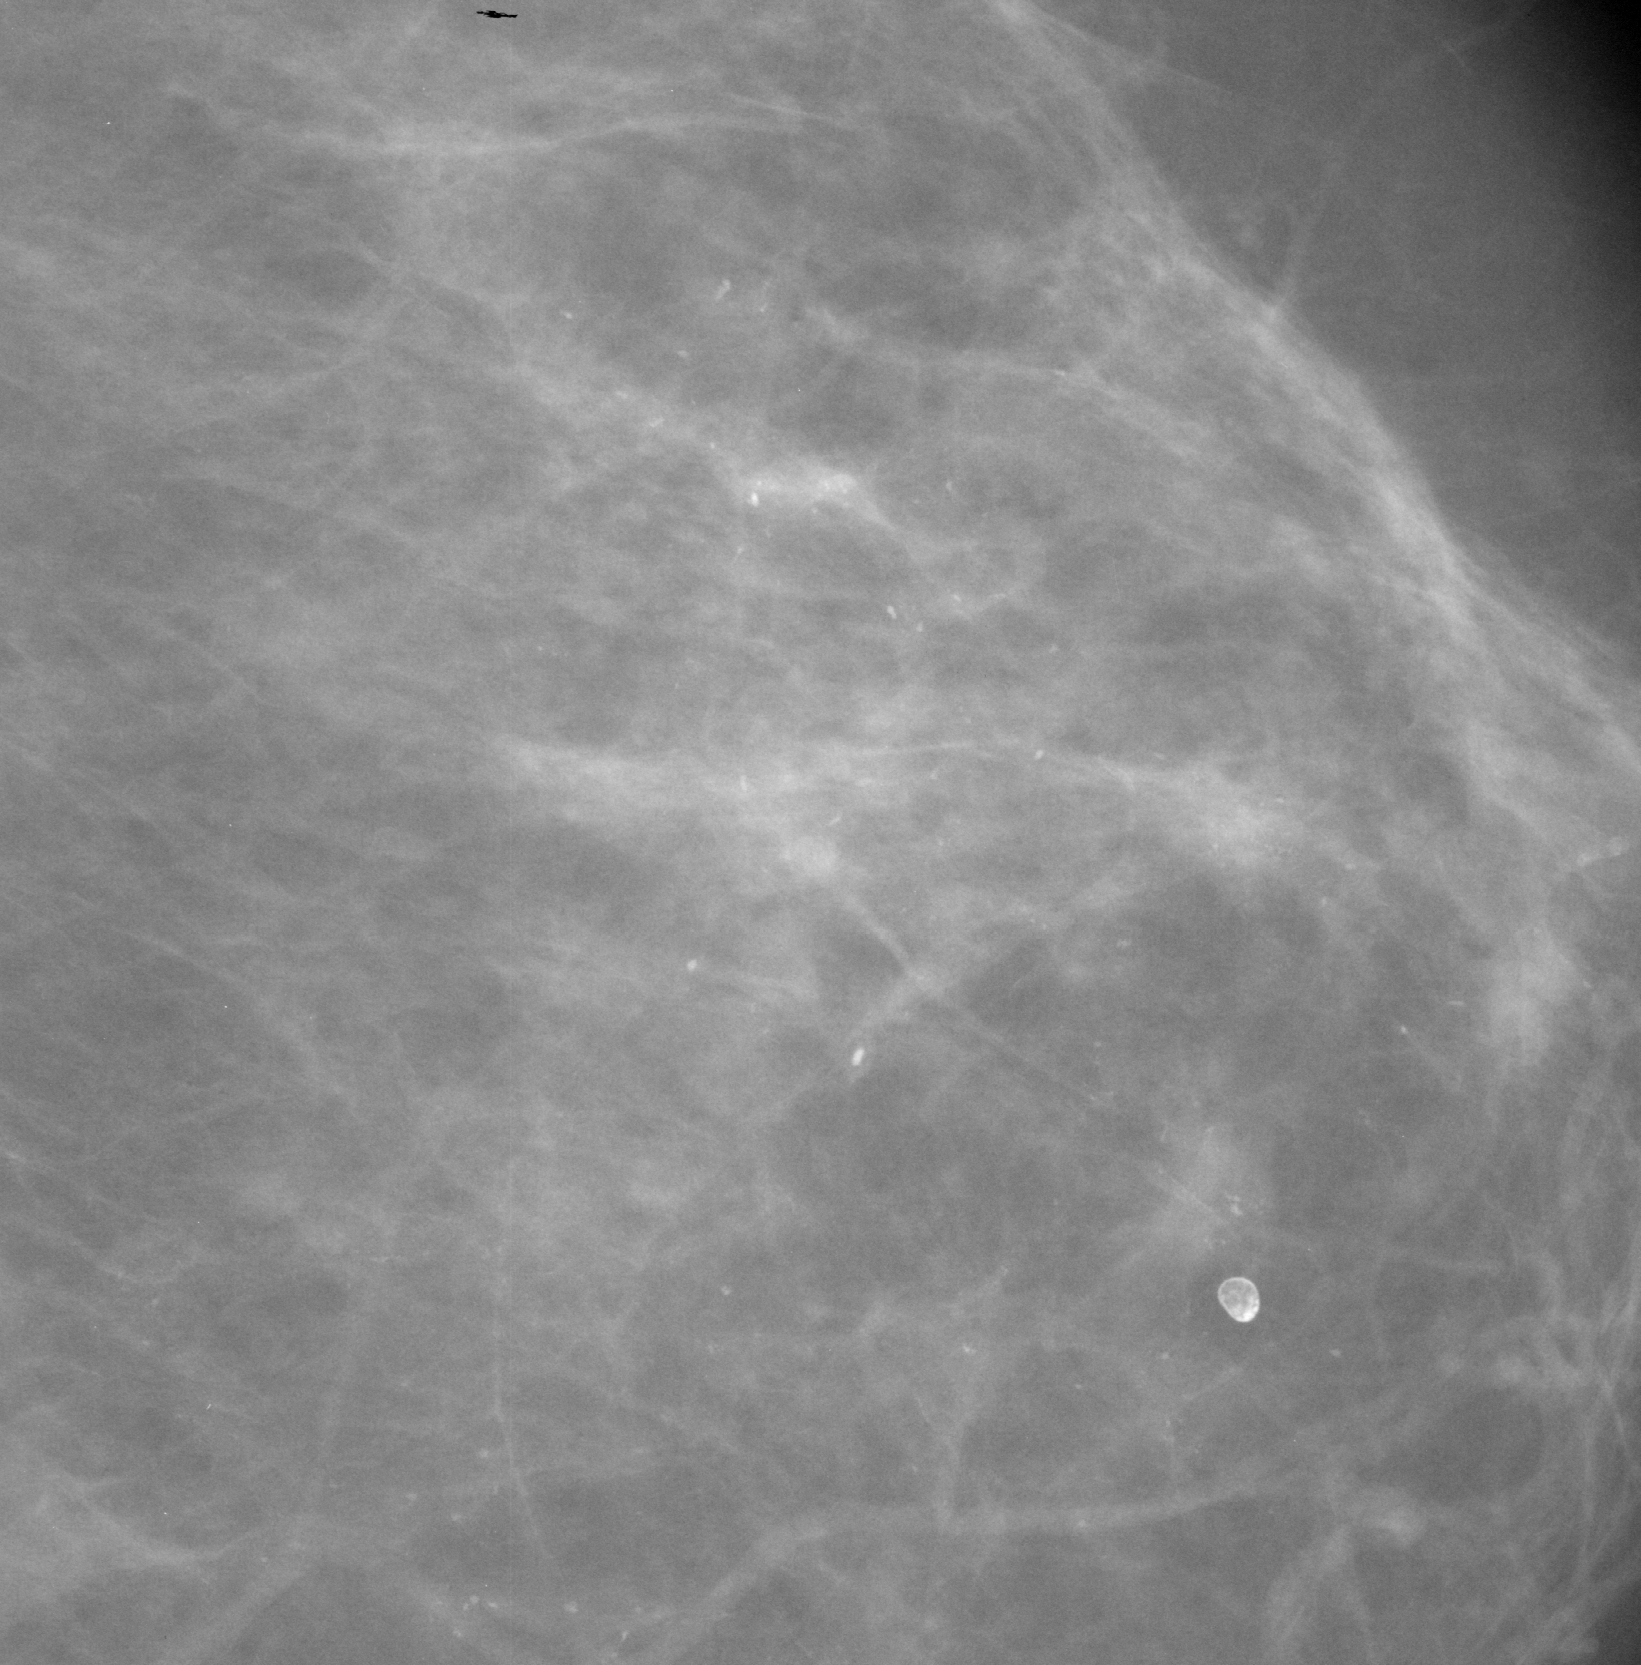
Crop from a digitized film mammogram around one marked abnormality, left breast, CC view.
- Calcifications, morphology amorphous, distribution regional; BI-RADS assessment category 5; pathology (as recorded): malignant.